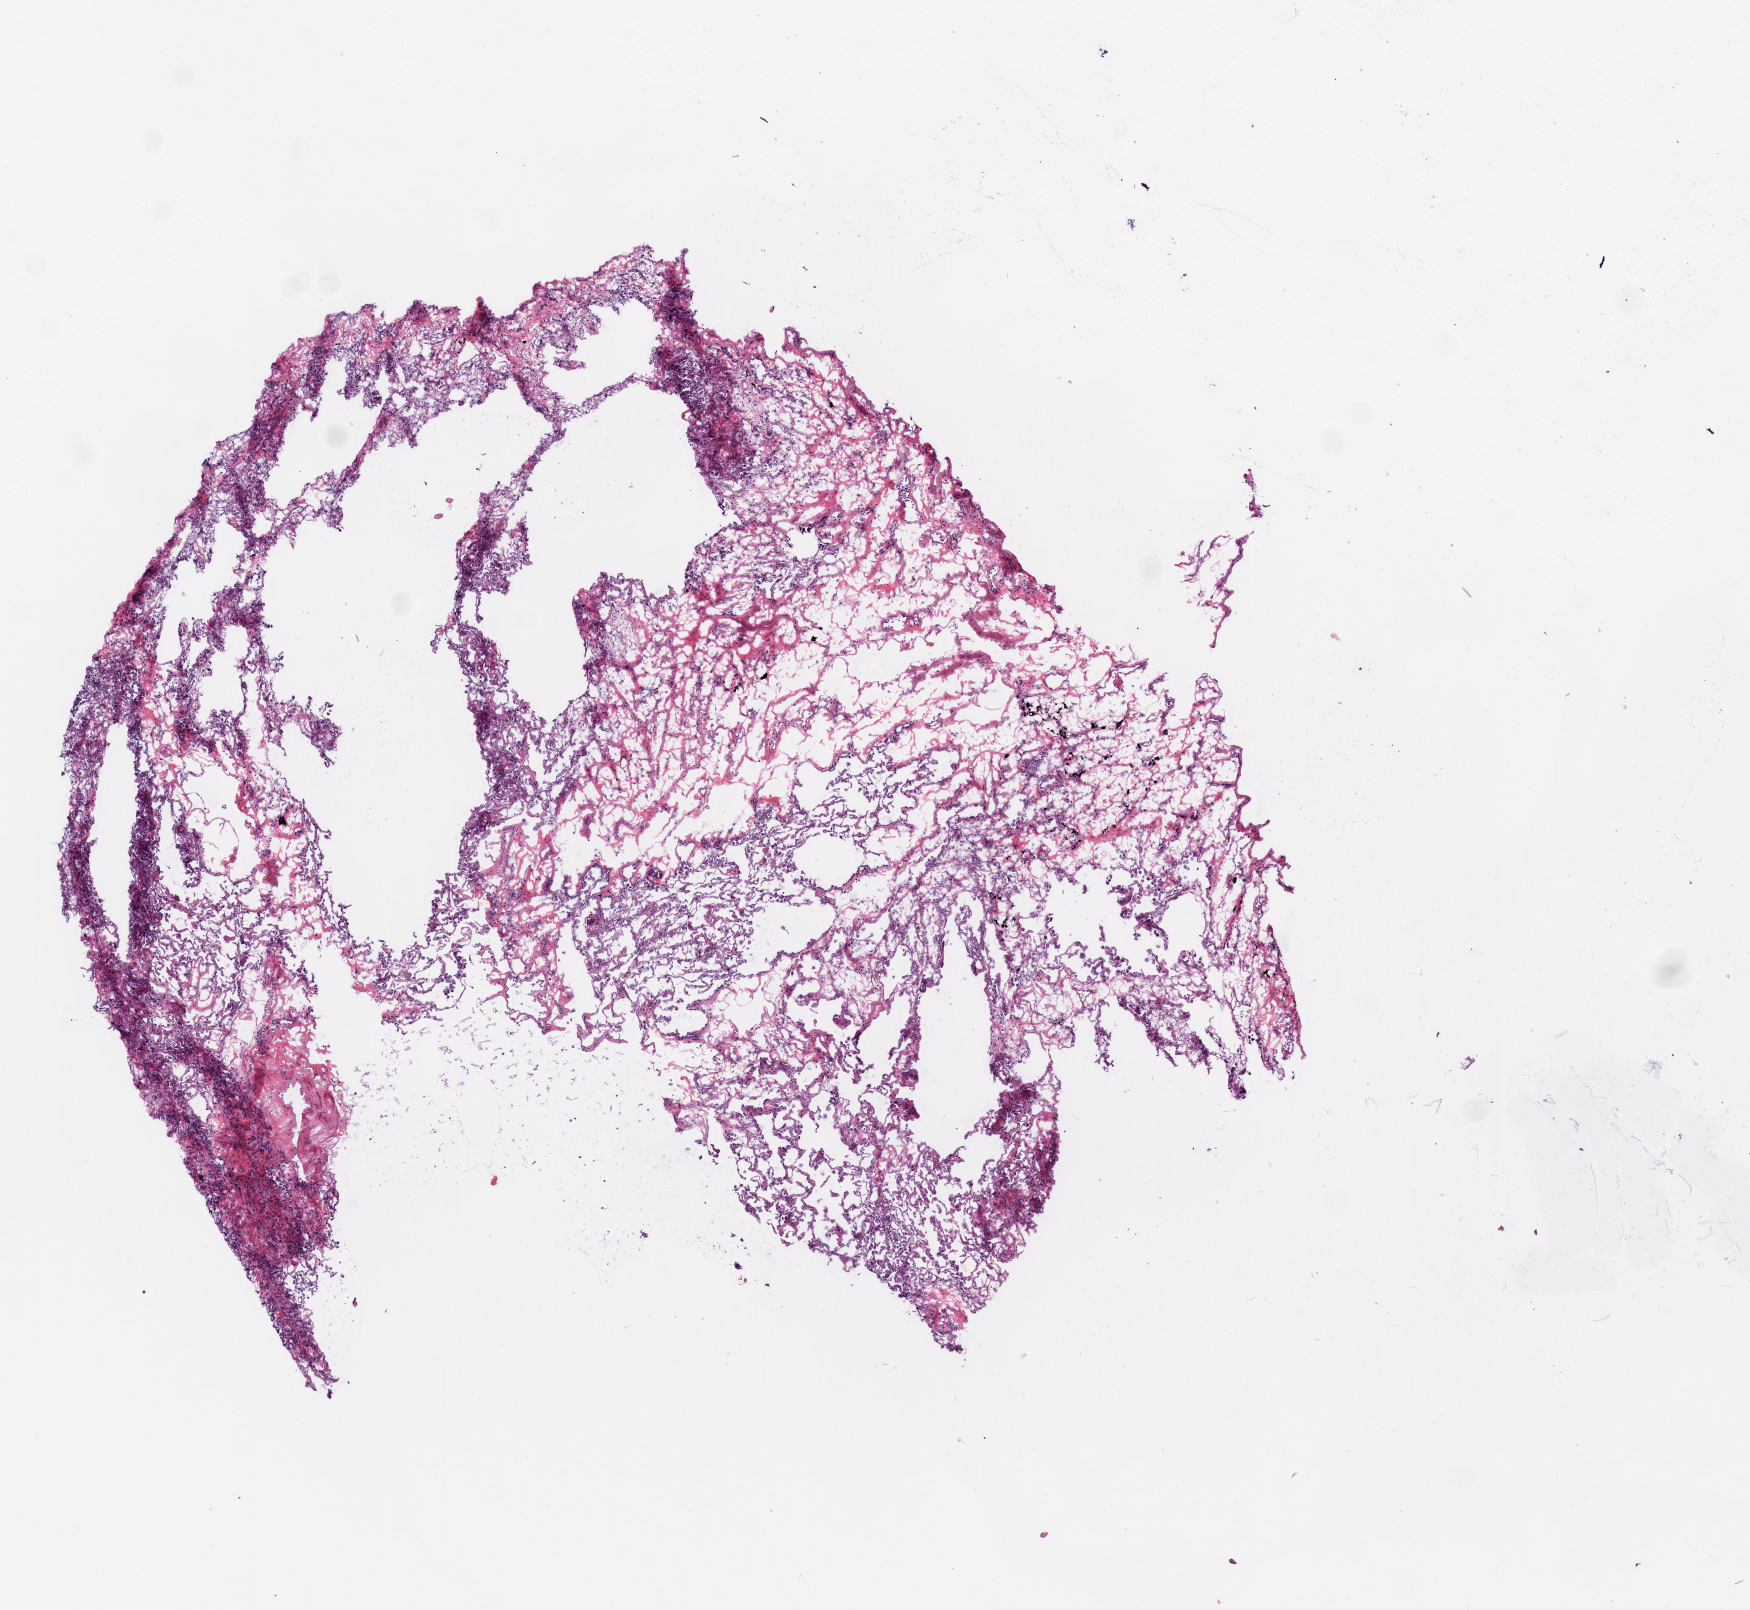
Whole-slide histology image, H&E-stained — shown as a low-resolution overview of the whole scanned area (about 7.0 x 6.5 mm, acquisition: 20x scan). Frozen section. Solid tissue normal (non-tumour tissue) sample from the lung. Patient: male, age at initial diagnosis 73 years.
This section: solid tissue normal sample (biorepository sample class). Patient diagnosis: Squamous cell carcinoma, NOS (lower lobe, lung).